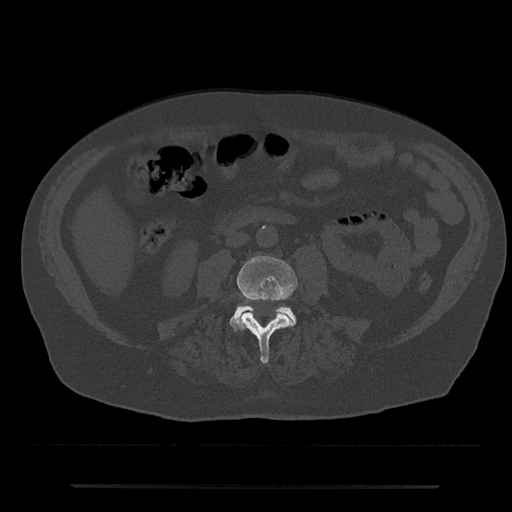
CT including the spine, one axial slice. Position 389 of 797 along the scan axis. 120 kVp. Bone window (W 1800 / L 400 HU). 0.5 mm slice thickness. 512 × 512 image matrix, field of view 434 × 434 mm. Male patient, age 80 years. Case-level facts recorded for this patient, not image findings: primary cancer: prostate.
Outlined on this slice (semi-automatically segmented with operator editing):
- L3 vertebra: bounding box <237,256,298,363> (left, top, right, bottom; pixels)
- L4 vertebra: <229,305,297,330>